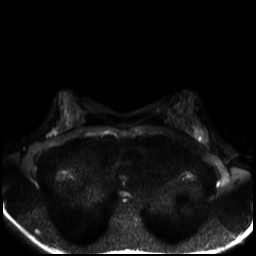
Breast MRI, one axial slice; slice 16 of 30 in the series (ordered by position); diffusion-weighted series; image 2 of 4 stored at this slice position (different b-values; order by instance number); 3 T; 256 × 256 image matrix. Female patient.
Annotated regions visible in this slice (outlined manually by an expert reader):
- tumour on diffusion-weighted imaging: bounding box (x1, y1, x2, y2) in pixels: (195, 130, 201, 136)